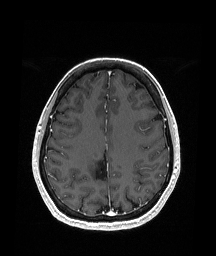
Brain MRI from a brain-tumour surgery series, one axial slice. Position 70 of 151 along the scan axis. T1-weighted post-contrast. 1.05 mm slice thickness. 216 × 256 image matrix, field of view 211 × 250 mm. Case-level facts recorded for this patient, not image findings: histopathology: Oligodendroglioma; WHO grade: 2; IDH mutation: yes; tumour location: Right Parietal.
Structures marked on this image (expert manual segmentation):
- previous resection cavity: bounding box <94,149,109,183> (left, top, right, bottom; pixels)